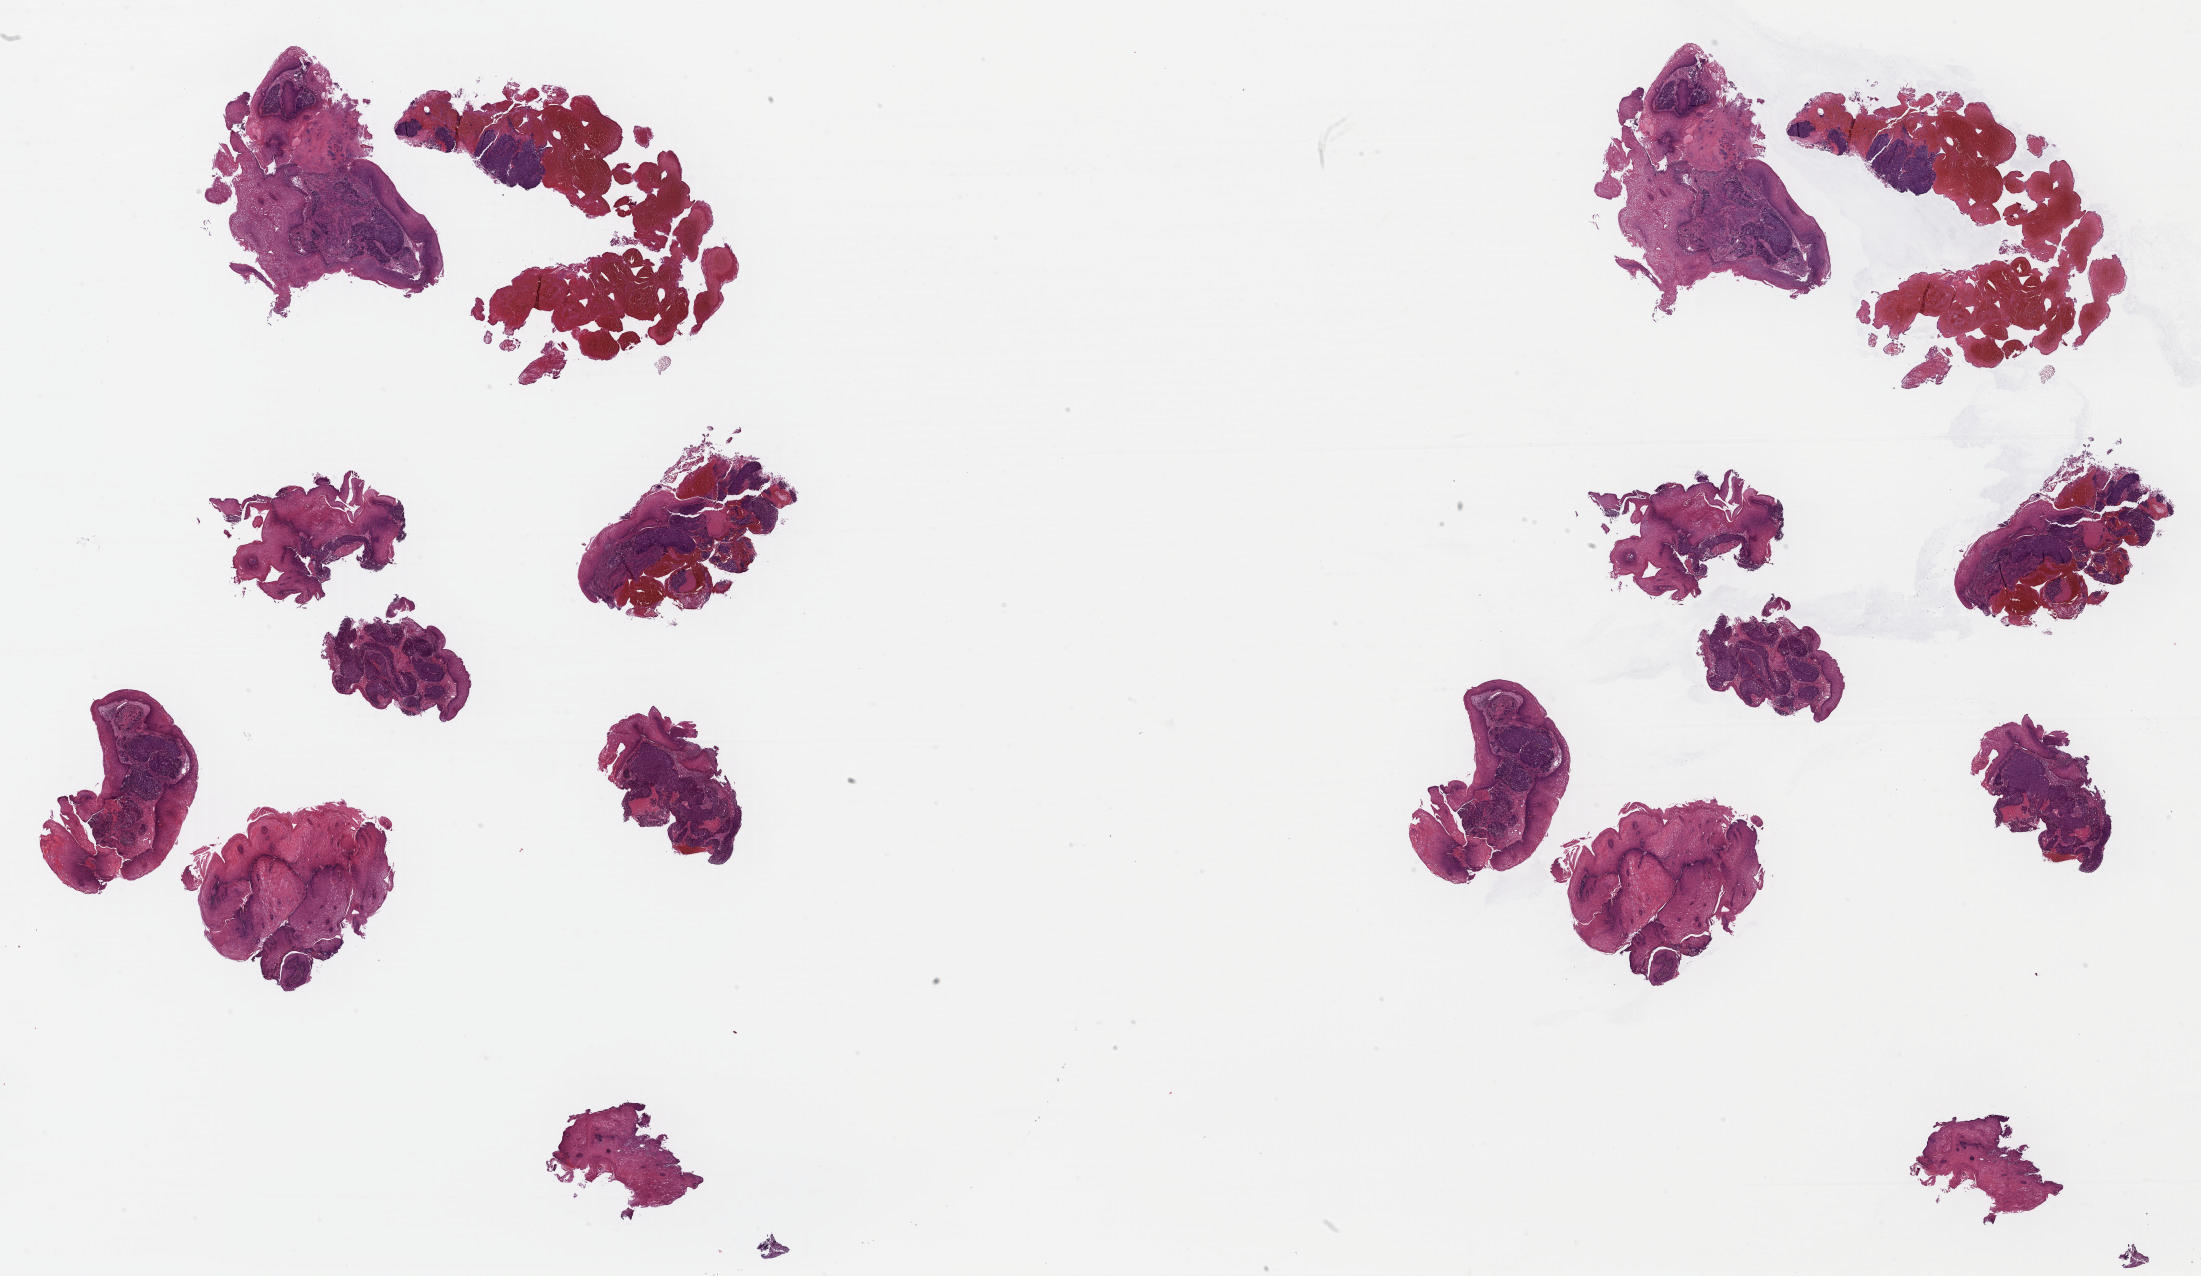
Whole-slide histology image, H&E — shown as a low-resolution overview of the whole scanned area (about 34.6 x 20.1 mm, slide scanned at 40x), FFPE section, sample: primary tumour, esophagus. Male, age 65 years at initial diagnosis. Histologic grade: G3 (poorly differentiated).
Histologic diagnosis: Squamous cell carcinoma, NOS (lower third of esophagus).